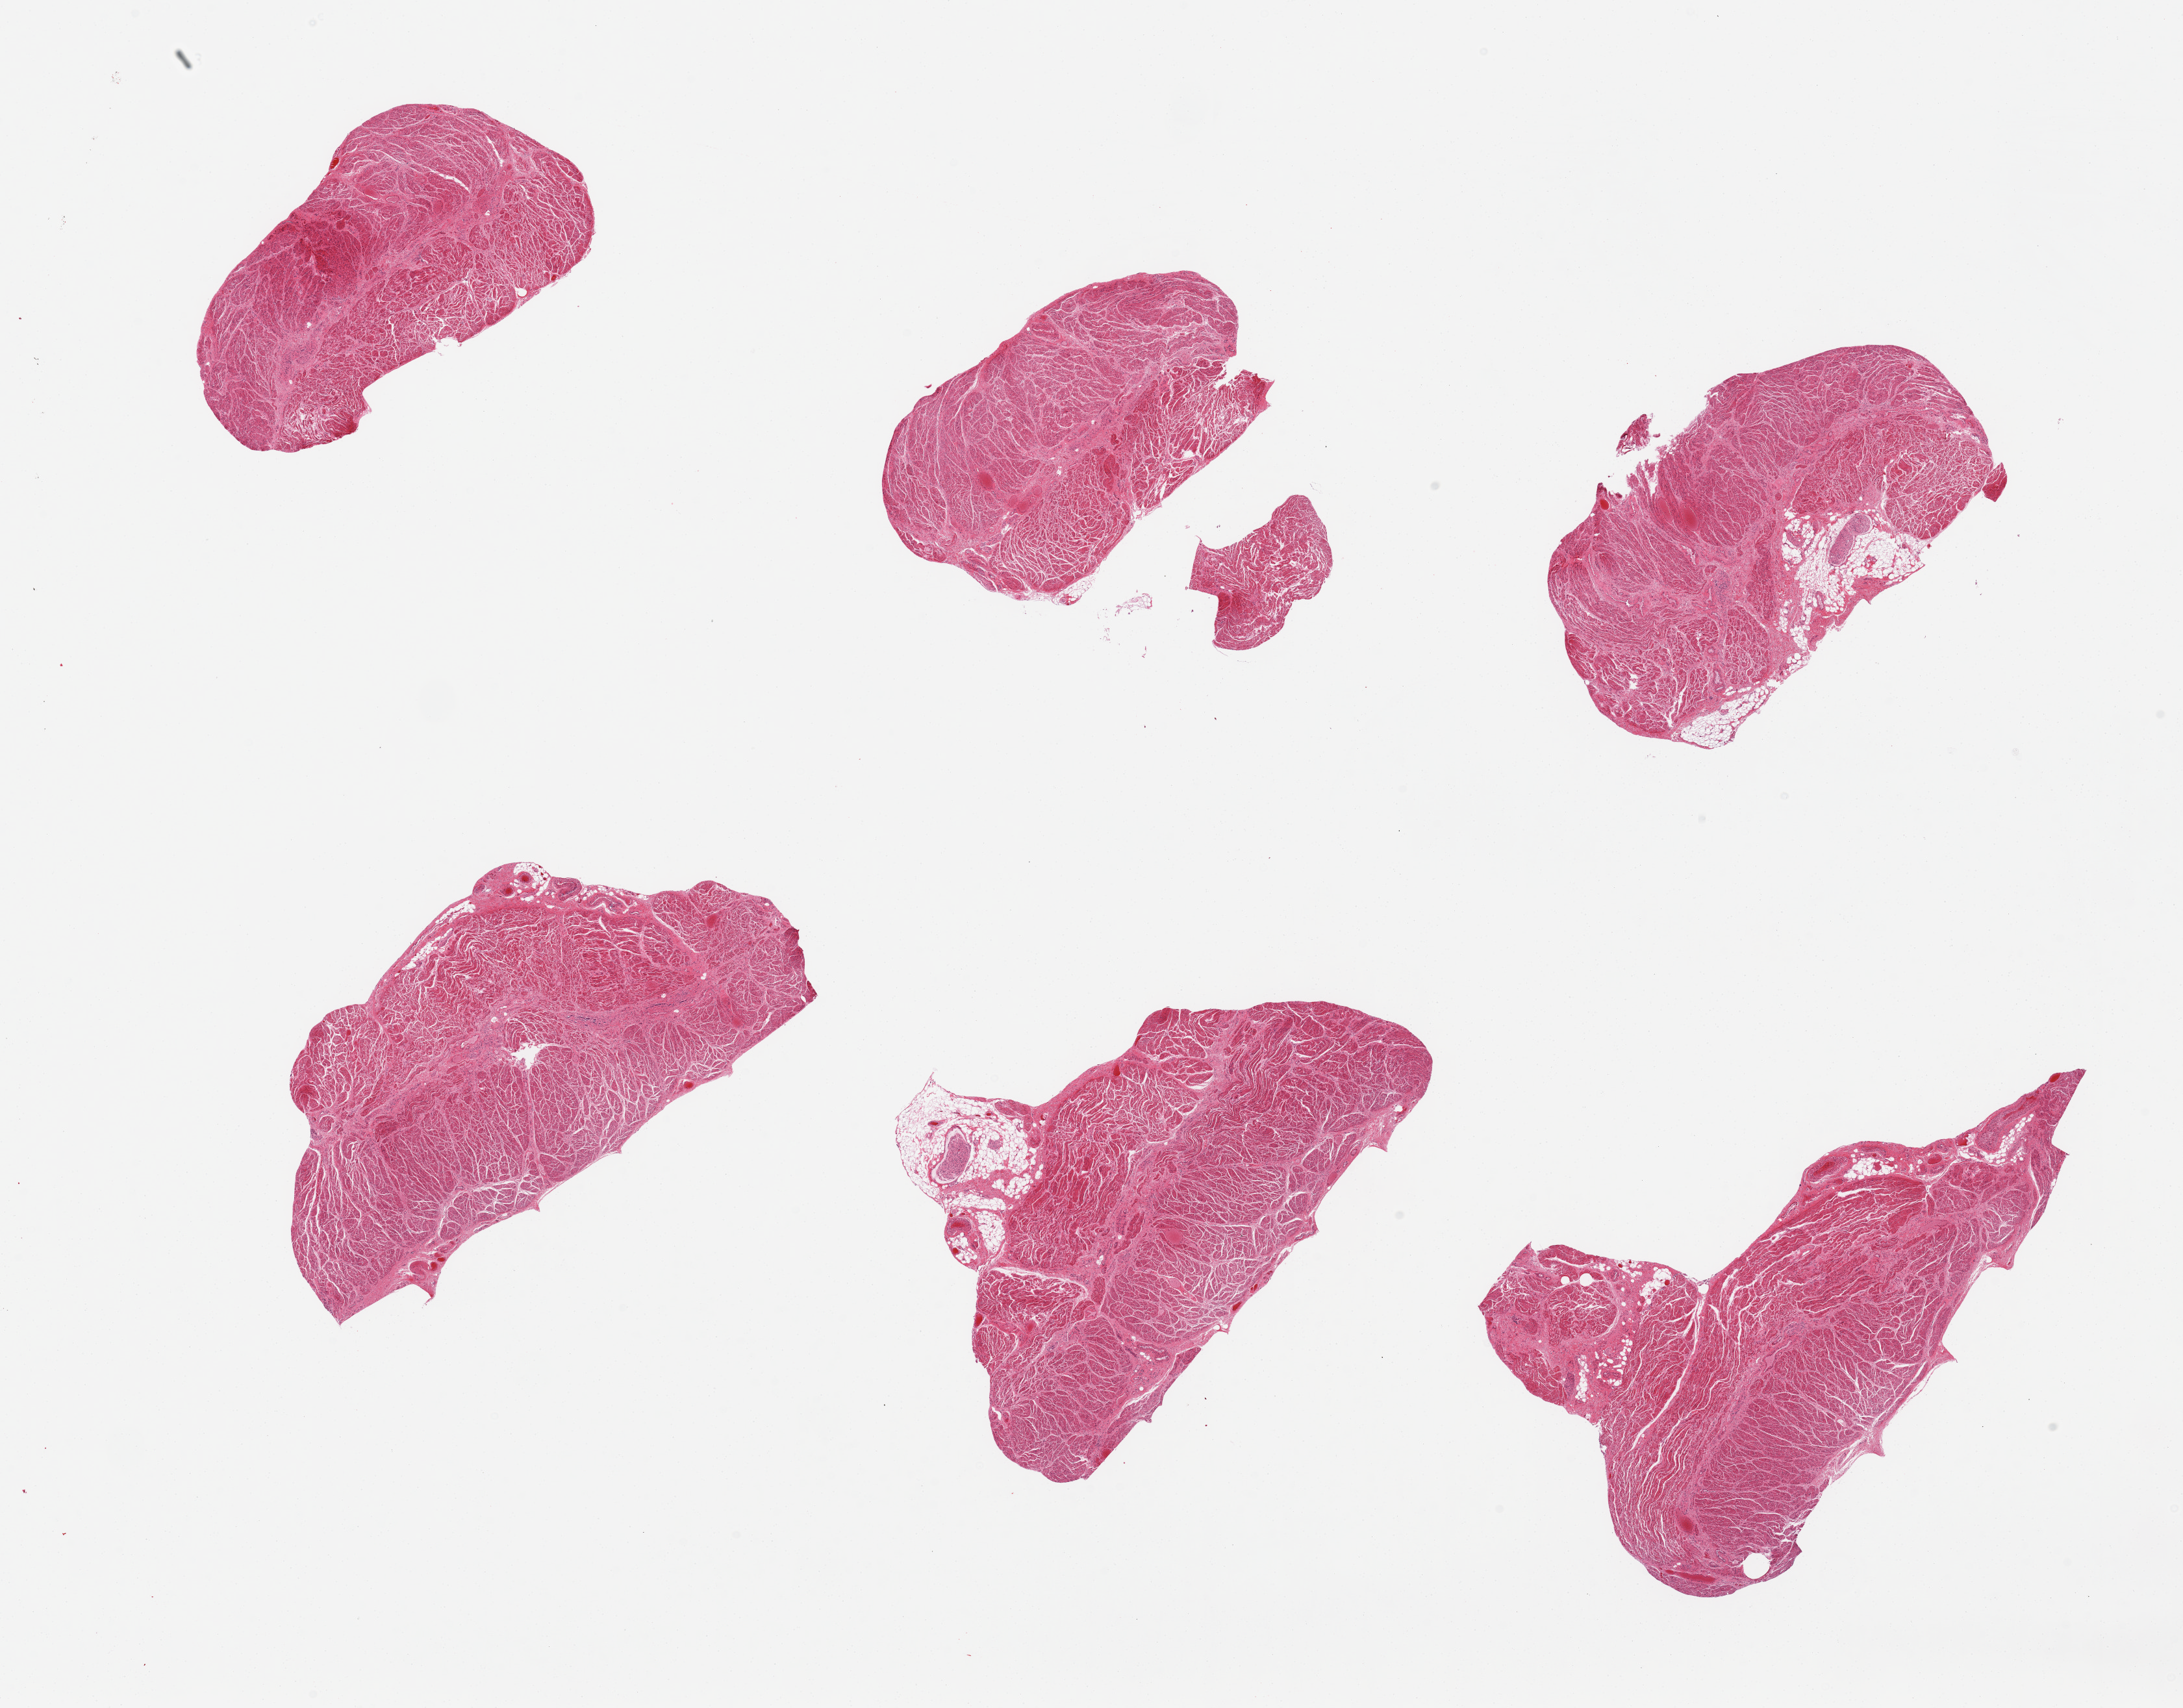
Digitized hematoxylin and eosin (H&E)-stained section — shown as a low-resolution overview of the whole scanned area (about 26.6 x 20.8 mm, from a 20x scan). PAXgene-fixed paraffin-embedded (PFPE) section. Target tissue: gastroesophageal junction. Donor tissue sample. Male donor.
Review note (as recorded): 6 pieces, small attachment of fat and nerve.